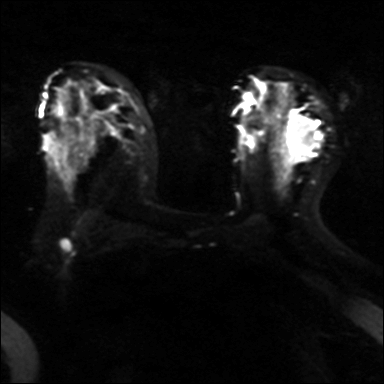
Breast MRI, one axial slice. Position 23 of 40 along the scan axis. Diffusion-weighted series; image 2 of 4 stored at this slice position (different b-values; order by instance number). 3 T. 4 mm slice thickness. 384 × 384 image matrix. Female patient.
Outlined on this slice (manually delineated by an expert):
- tumour on diffusion-weighted imaging: bounding box (x1, y1, x2, y2) in pixels: (292, 112, 321, 147)